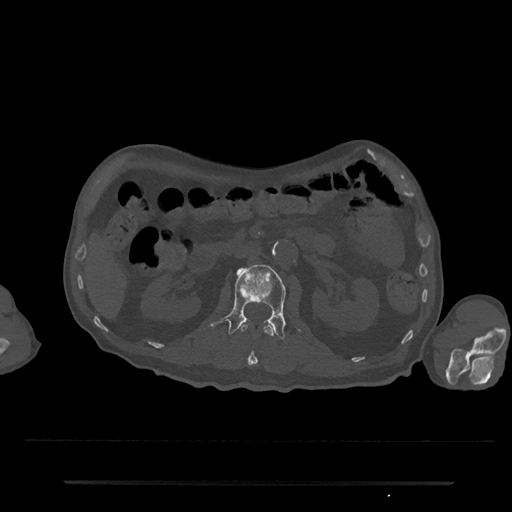
CT including the spine, one axial slice; position 82 of 797 along the scan axis; reconstruction kernel Br40s/3; 120 kVp; bone window (W 1800 / L 400 HU); 0.5 mm slice thickness; 512 × 512 image matrix, field of view 427 × 427 mm. Patient: male, 74 years. From the clinical record (not read from this slice): primary cancer: prostate.
Structures marked on this image (semi-automatically segmented with operator editing):
- L1 vertebra: bounding box [x1, y1, x2, y2] px = [239, 323, 275, 367]
- L2 vertebra: [210, 264, 286, 340]